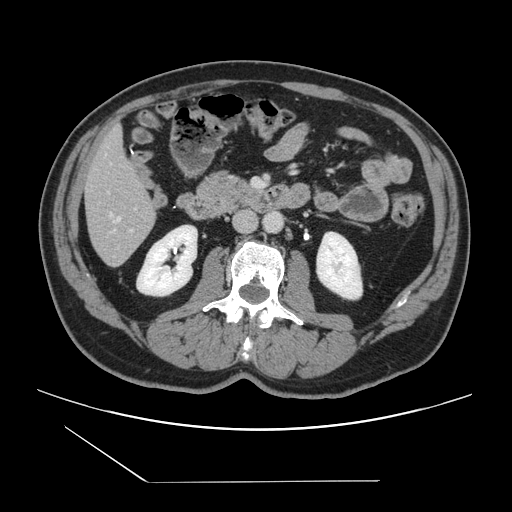
Contrast-enhanced abdominal CT, one axial slice. Slice 42 of 157 in the series (ordered by position). 120 kVp. Intravenous contrast given. Soft-tissue window (W 400 / L 40 HU). 2.5 mm slice thickness. 512 × 512 image matrix, field of view 407 × 407 mm. Male patient, age 61 years. From the clinical record (not read from this slice): diagnosis: colorectal cancer liver metastases, imaged before liver resection; multiple liver metastases: yes; largest metastasis: 5.5 cm; chemotherapy before resection: no.
Structures marked on this image (manually delineated by an expert):
- hepatic veins: bounding box [x1, y1, x2, y2] px = [111, 214, 120, 221]
- liver: [85, 130, 156, 266]
- planned liver remnant (the part of the liver to remain after resection): [85, 130, 153, 218]
- portal vein (with intrahepatic branches): [113, 219, 133, 231]